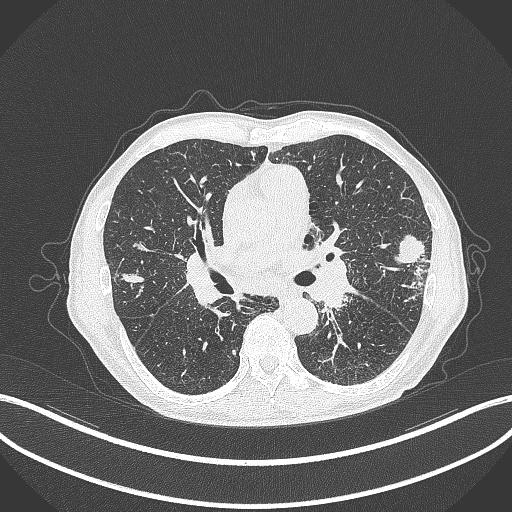
Chest CT, one axial slice; position 224 of 463 along the scan axis; 120 kVp; lung window (W 1500 / L -600 HU); 1 mm slice thickness; 512 × 512 image matrix, field of view 400 × 400 mm. Male patient, age 74 years. Case-level facts recorded for this patient, not image findings: clinical TNM (as recorded): T2a N1 M0.
Structures marked on this image (bounding box drawn by a radiologist):
- lung tumour (recorded histology: adenocarcinoma): bounding box [x1, y1, x2, y2] px = [394, 233, 430, 268]